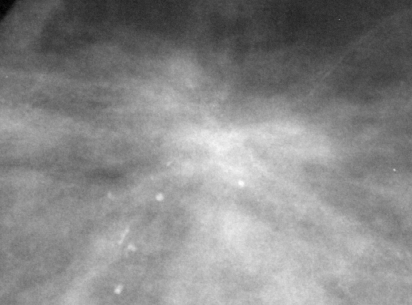
Region of interest cut from a scanned film mammogram (one marked finding); right breast; CC view.
Mass, shape architectural distortion, margins ill defined / spiculated; BI-RADS assessment category 4; subtlety rating 3 on a 1 (subtle) to 5 (obvious) scale; pathology result (as recorded, not read from the image): malignant.